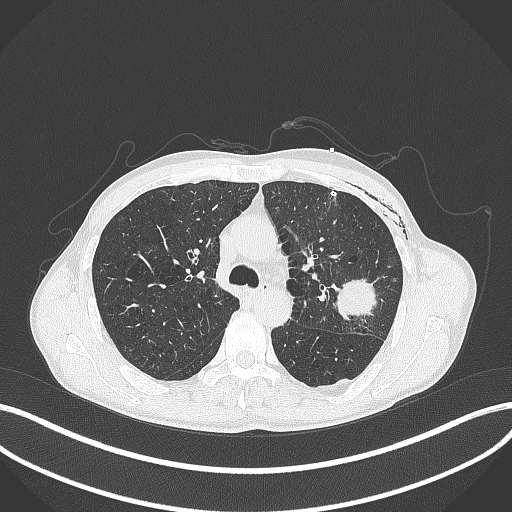
Chest CT, one axial slice. Slice 272 of 457 in the series (ordered by position). Reconstruction kernel B70f. 120 kVp. Lung window (W 1500 / L -600 HU). 512 × 512 image matrix. Male patient, age 58 years. From the clinical record (not read from this slice): clinical TNM (as recorded): T3 N0 M0.
Structures marked on this image (bounding box drawn by a radiologist):
- lung tumour (recorded histology: adenocarcinoma): box from (x=335, y=275) to (x=379, y=326) px